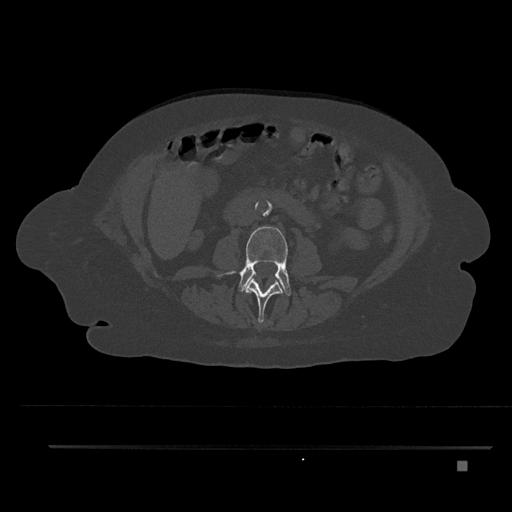
CT including the spine, one axial slice. Slice 147 of 797 in the series (ordered by position). Reconstruction kernel Br40s/3. Bone window (W 1800 / L 400 HU). 512 × 512 image matrix. Patient: female, 76 years. Case-level facts recorded for this patient, not image findings: primary cancer: lung.
Structures marked on this image (semi-automatic segmentation, software-assisted and operator-edited):
- L2 vertebra: bounding box (x1, y1, x2, y2) in pixels: (245, 279, 283, 324)
- L3 vertebra: (230, 226, 292, 296)